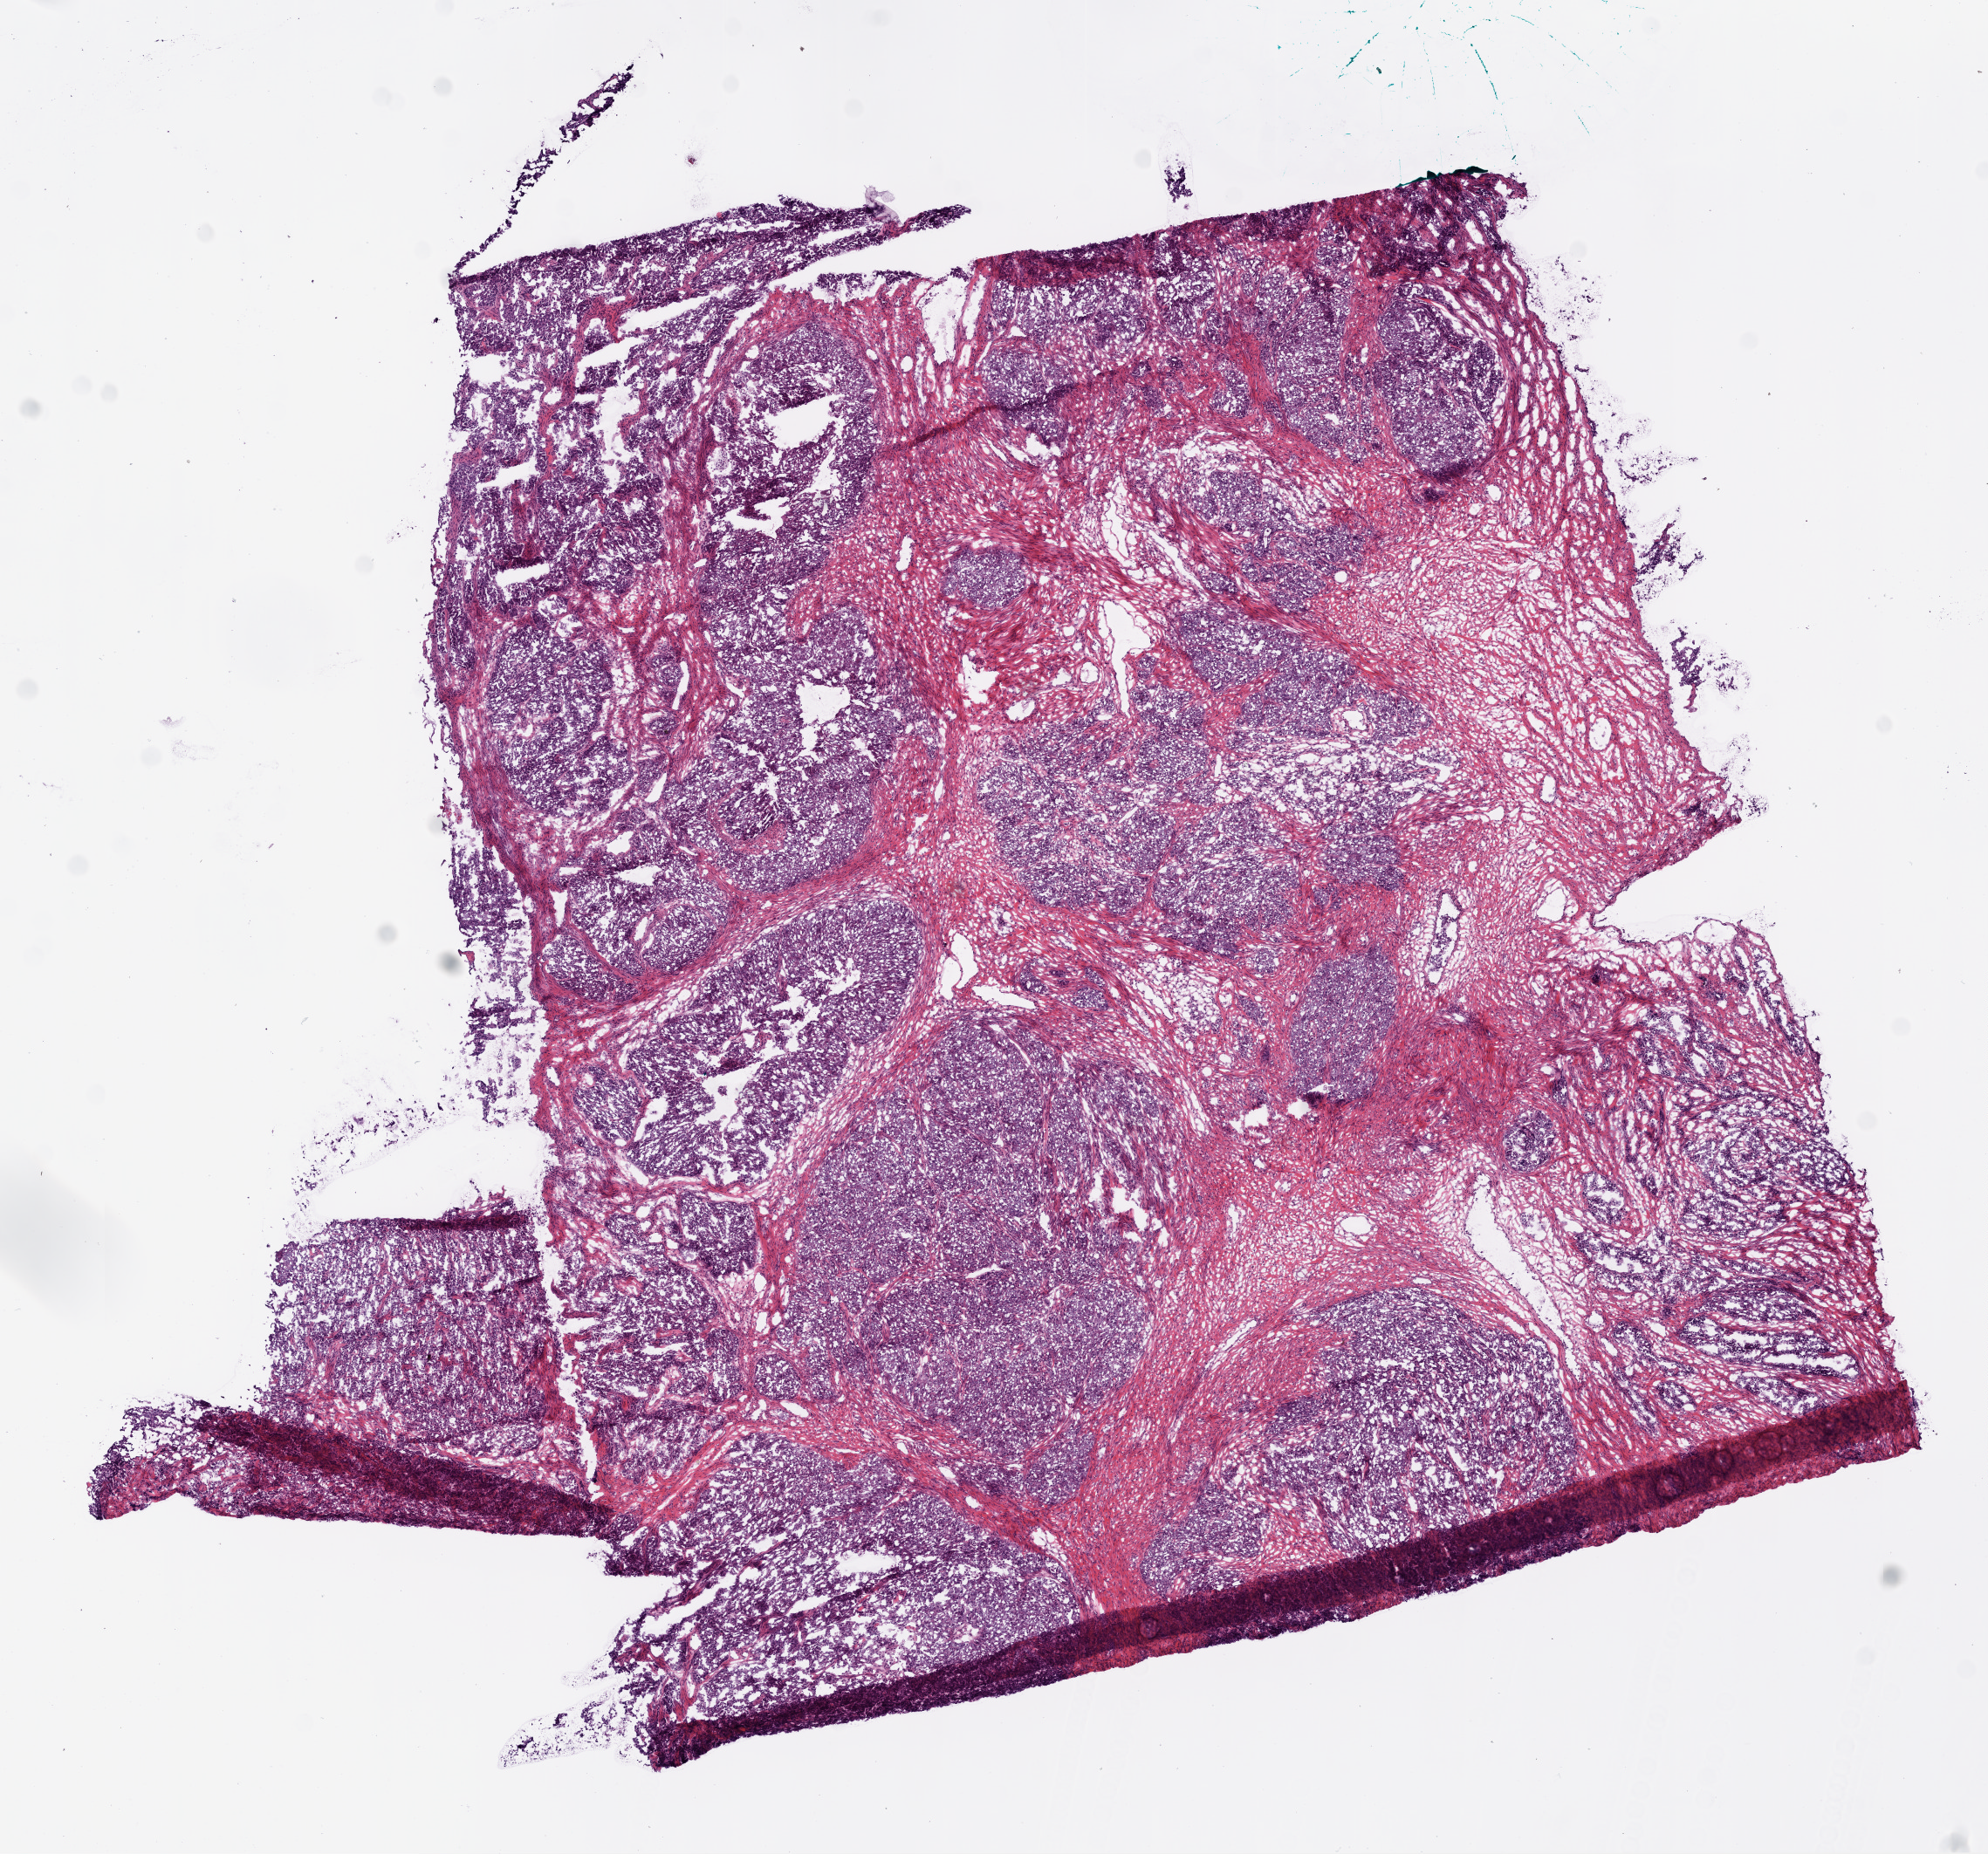
Digitized H&E-stained tissue section (whole slide), low-resolution overview of the scanned area, about 9.2 x 8.6 mm, frozen section from the bottom of the tissue portion, primary tumour sample from the ovary. Female patient; age at initial diagnosis 57 years. Histologic grade: G3 (poorly differentiated). Composition of this section per pathologist review: tumour cells 69%, tumour nuclei 80%, normal cells 0%, stromal cells 30%, necrosis 1%.
Histologic diagnosis: Serous cystadenocarcinoma, NOS. Laterality: bilateral. FIGO stage: IIIB.